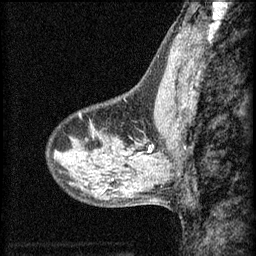
Breast MRI (dynamic contrast-enhanced), one sagittal slice; slice 21 of 60 in the series (ordered by position); 3 images stored at this slice position (order not interpretable as contrast timing); 1.5 T; TE 4.2 ms, TR 8.2 ms; 256 × 256 image matrix, field of view 180 × 180 mm. Female patient, age 40 years.
Outlined on this slice (semi-automatic segmentation, software-assisted and operator-edited):
- analysis volume of interest (the breast-tissue region the enhancement analysis was run in; not a lesion): bounding box (x1, y1, x2, y2) in pixels: (104, 116, 159, 165)
- tumour enhancement mask (voxels above the 70 % enhancement threshold inside the analysis volume of interest): (130, 144, 155, 159)